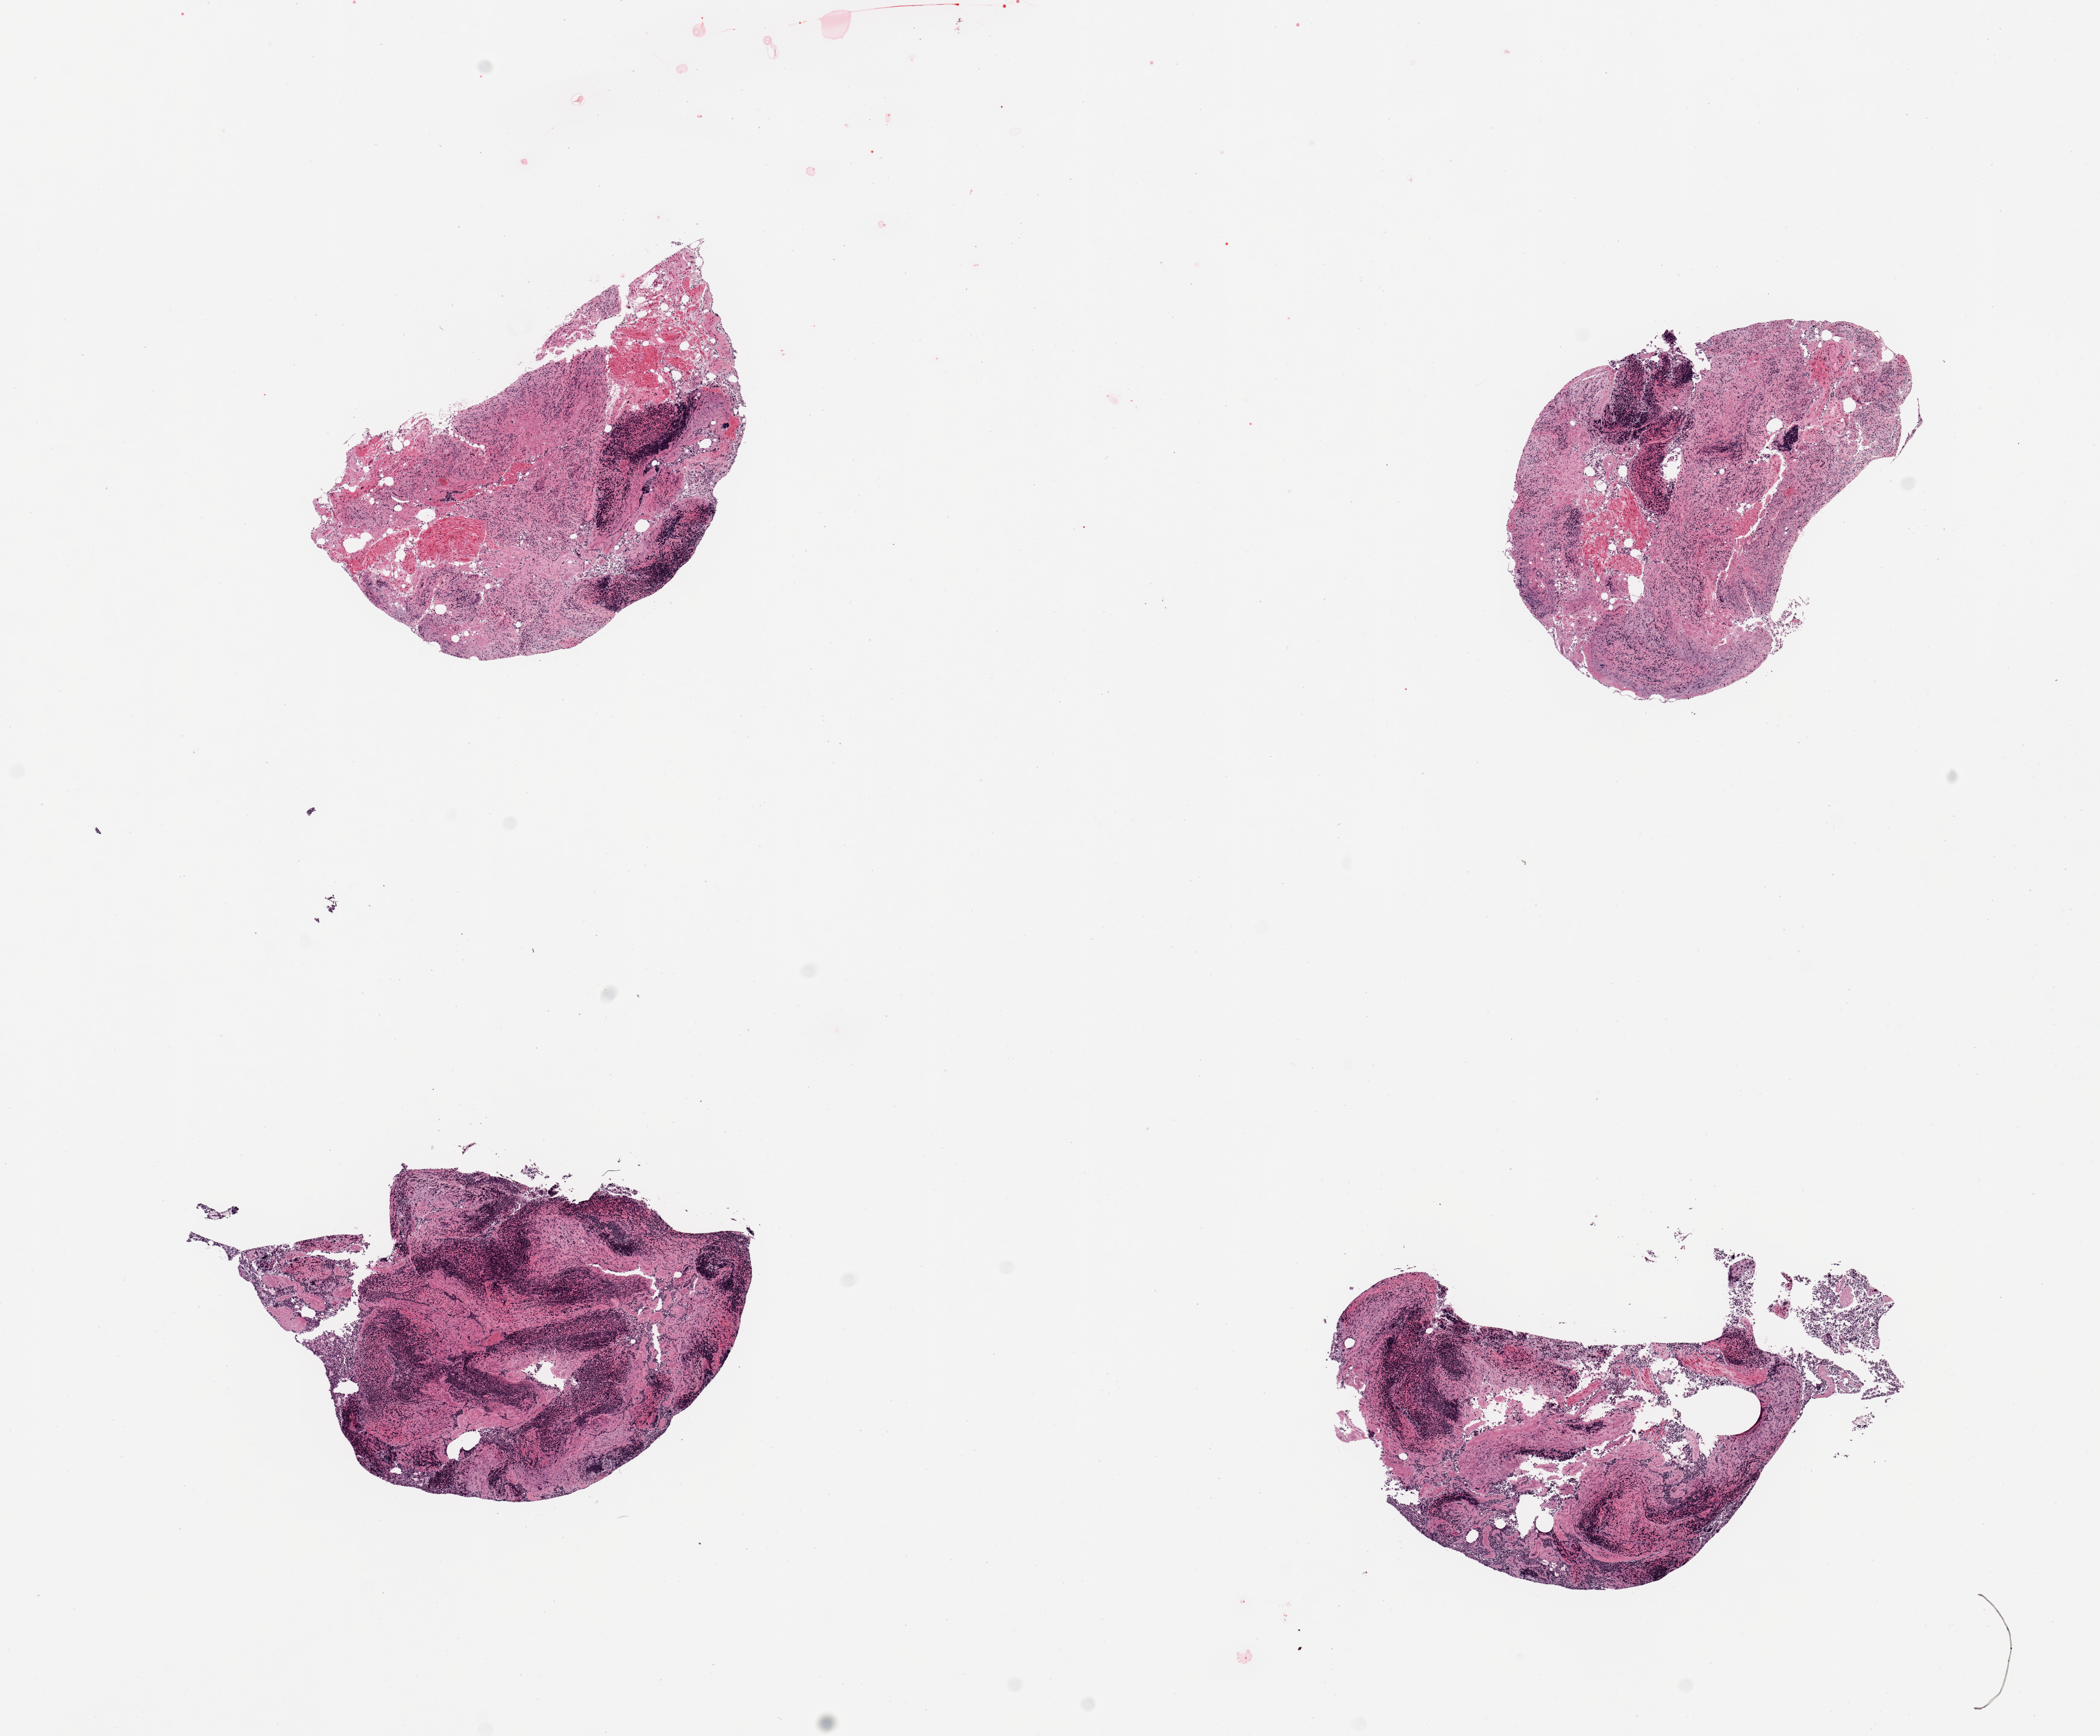
Hematoxylin and eosin (H&E) whole-slide image — a low-resolution overview of the entire scanned area, about 13.8 x 11.4 mm (slide scanned at 20x). PAXgene-fixed, paraffin-embedded tissue. Section of ileum (target tissue). Donor tissue sample. Donor sex: female.
Reviewer comment on this tissue sample: 4 pieces, mucosa markedly autolyzed, residual target lymphoid elements, ~20-30% total.